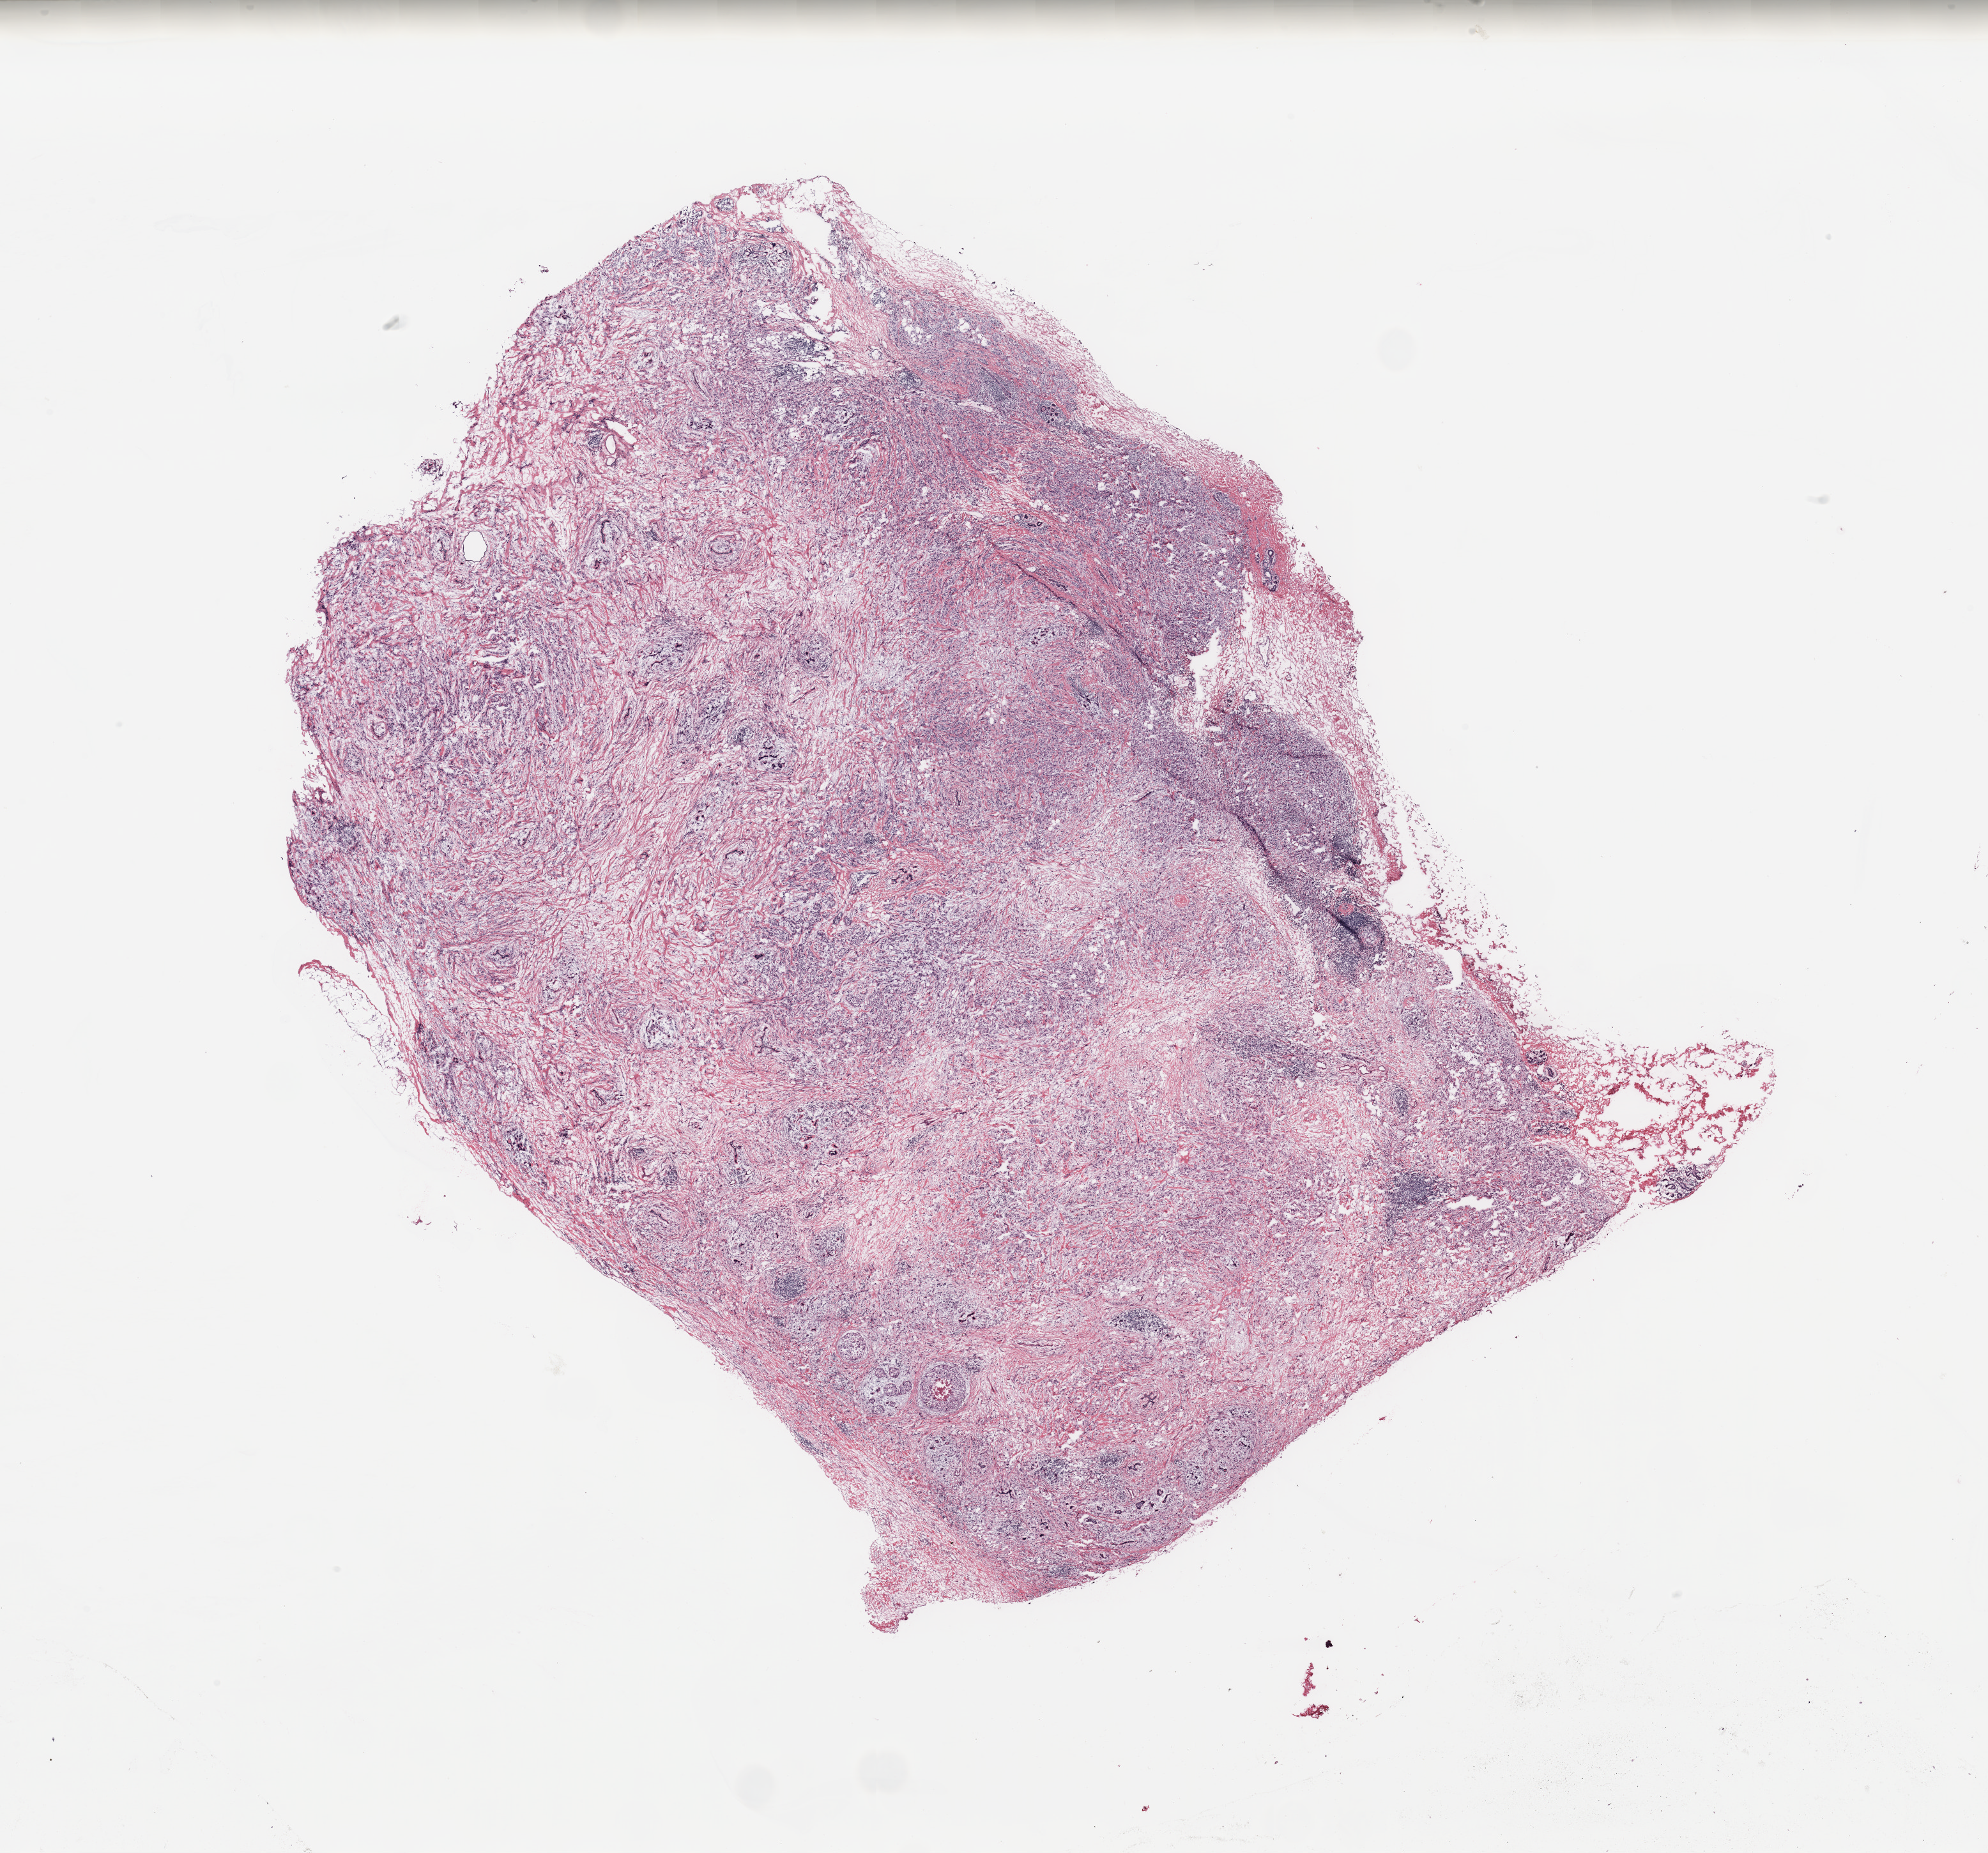
Digitized Hematoxylin and eosin (H&E) stained tissue section (whole slide), low-resolution overview of the scanned area, about 24.6 x 22.9 mm; breast, tissue type not recorded.
• patient diagnosis (cohort enrolment): breast cancer (breast)